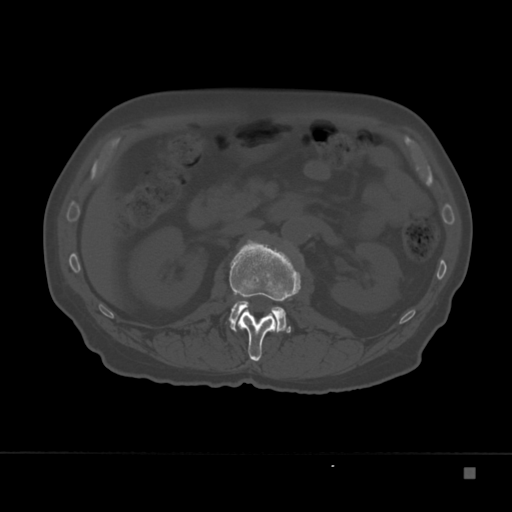
CT including the spine, one axial slice; position 103 of 332 along the scan axis; bone window (W 1800 / L 400 HU); 1.5 mm slice thickness; 512 × 512 image matrix, field of view 389 × 389 mm. Male patient, age 72 years. Case-level facts recorded for this patient, not image findings: primary cancer: skeletal.
Outlined on this slice (semi-automatically segmented with operator editing):
- L1 vertebra: bounding box (x1, y1, x2, y2) in pixels: (230, 239, 301, 362)
- L2 vertebra: (229, 301, 291, 333)